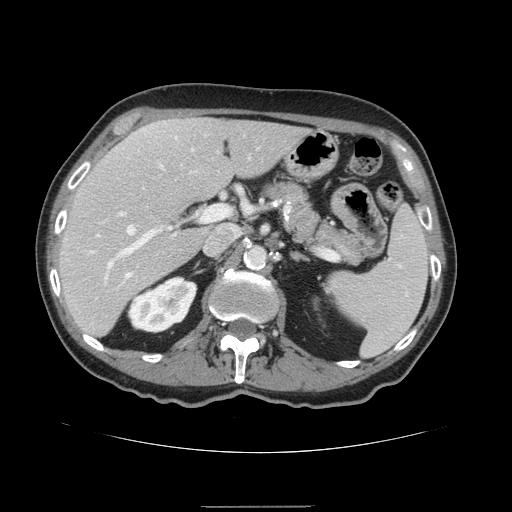
Contrast-enhanced abdominal CT, one axial slice. Slice 89 of 168 in the series (ordered by position). 120 kVp. Intravenous contrast given. Soft-tissue window (W 400 / L 40 HU). 2.5 mm slice thickness. 512 × 512 image matrix. Male patient, age 74 years. Case-level facts recorded for this patient, not image findings: diagnosis: colorectal cancer liver metastases, imaged before liver resection; multiple liver metastases: no; largest metastasis: 14.5 cm; disease in both lobes: yes.
Structures marked on this image (expert manual segmentation):
- hepatic veins: box from (x=127, y=225) to (x=135, y=276) px
- liver: (x=59, y=118)–(x=310, y=337)
- planned liver remnant (the part of the liver to remain after resection): (x=59, y=120)–(x=311, y=337)
- portal vein (with intrahepatic branches): (x=87, y=208)–(x=228, y=270)